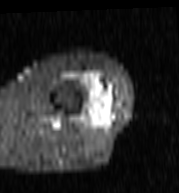
MRI of an extremity soft-tissue mass, one axial slice. Slice 29 of 103 in the series (ordered by position). STIR. MR volume resampled by the dataset authors to the PET/CT grid (not the native acquisition matrix). 3.27 mm slice thickness. 179 × 193 image matrix, field of view 175 × 188 mm. Female patient. From the clinical record (not read from this slice): histological type: undifferentiated – high grade; grade: high; site of the primary tumour: left thigh.
Annotated regions visible in this slice (expert contour drawn on MRI and transferred to this co-registered scan by the dataset authors):
- gross tumour volume including surrounding oedema: bounding box [x1, y1, x2, y2] px = [66, 73, 115, 116]